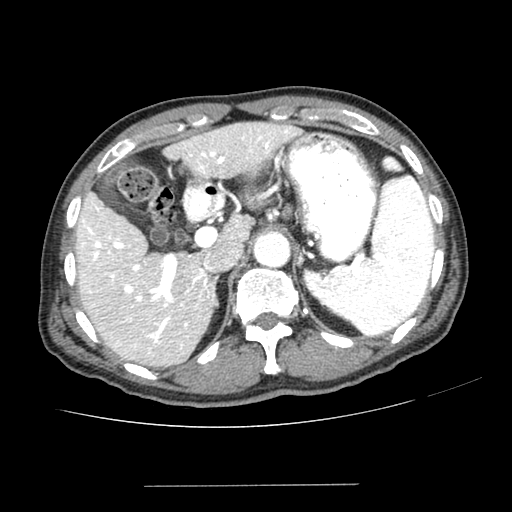
Contrast-enhanced abdominal CT (liver protocol), one axial slice; position 157 of 187 along the scan axis; reconstruction kernel SOFT; one of 2 acquisitions stored at this slice position; soft-tissue window (W 400 / L 40 HU); 512 × 512 image matrix, field of view 360 × 360 mm. From the clinical record (not read from this slice): diagnosis: hepatocellular carcinoma (patient treated with transarterial chemoembolisation; whether this scan precedes or follows treatment is not stated here); TNM stage (as recorded): Stage-I; Child-Pugh class: A; tumour differentiation: poorly differentiated; tumour nodularity: uninodular.
Annotated regions visible in this slice (semi-automatically segmented with operator editing):
- liver parenchyma outside the tumour (the mass and vessels are separate outlines, so this box may not span the whole liver): box from (x=76, y=122) to (x=298, y=366) px
- liver vessels: (x=81, y=130)–(x=289, y=350)